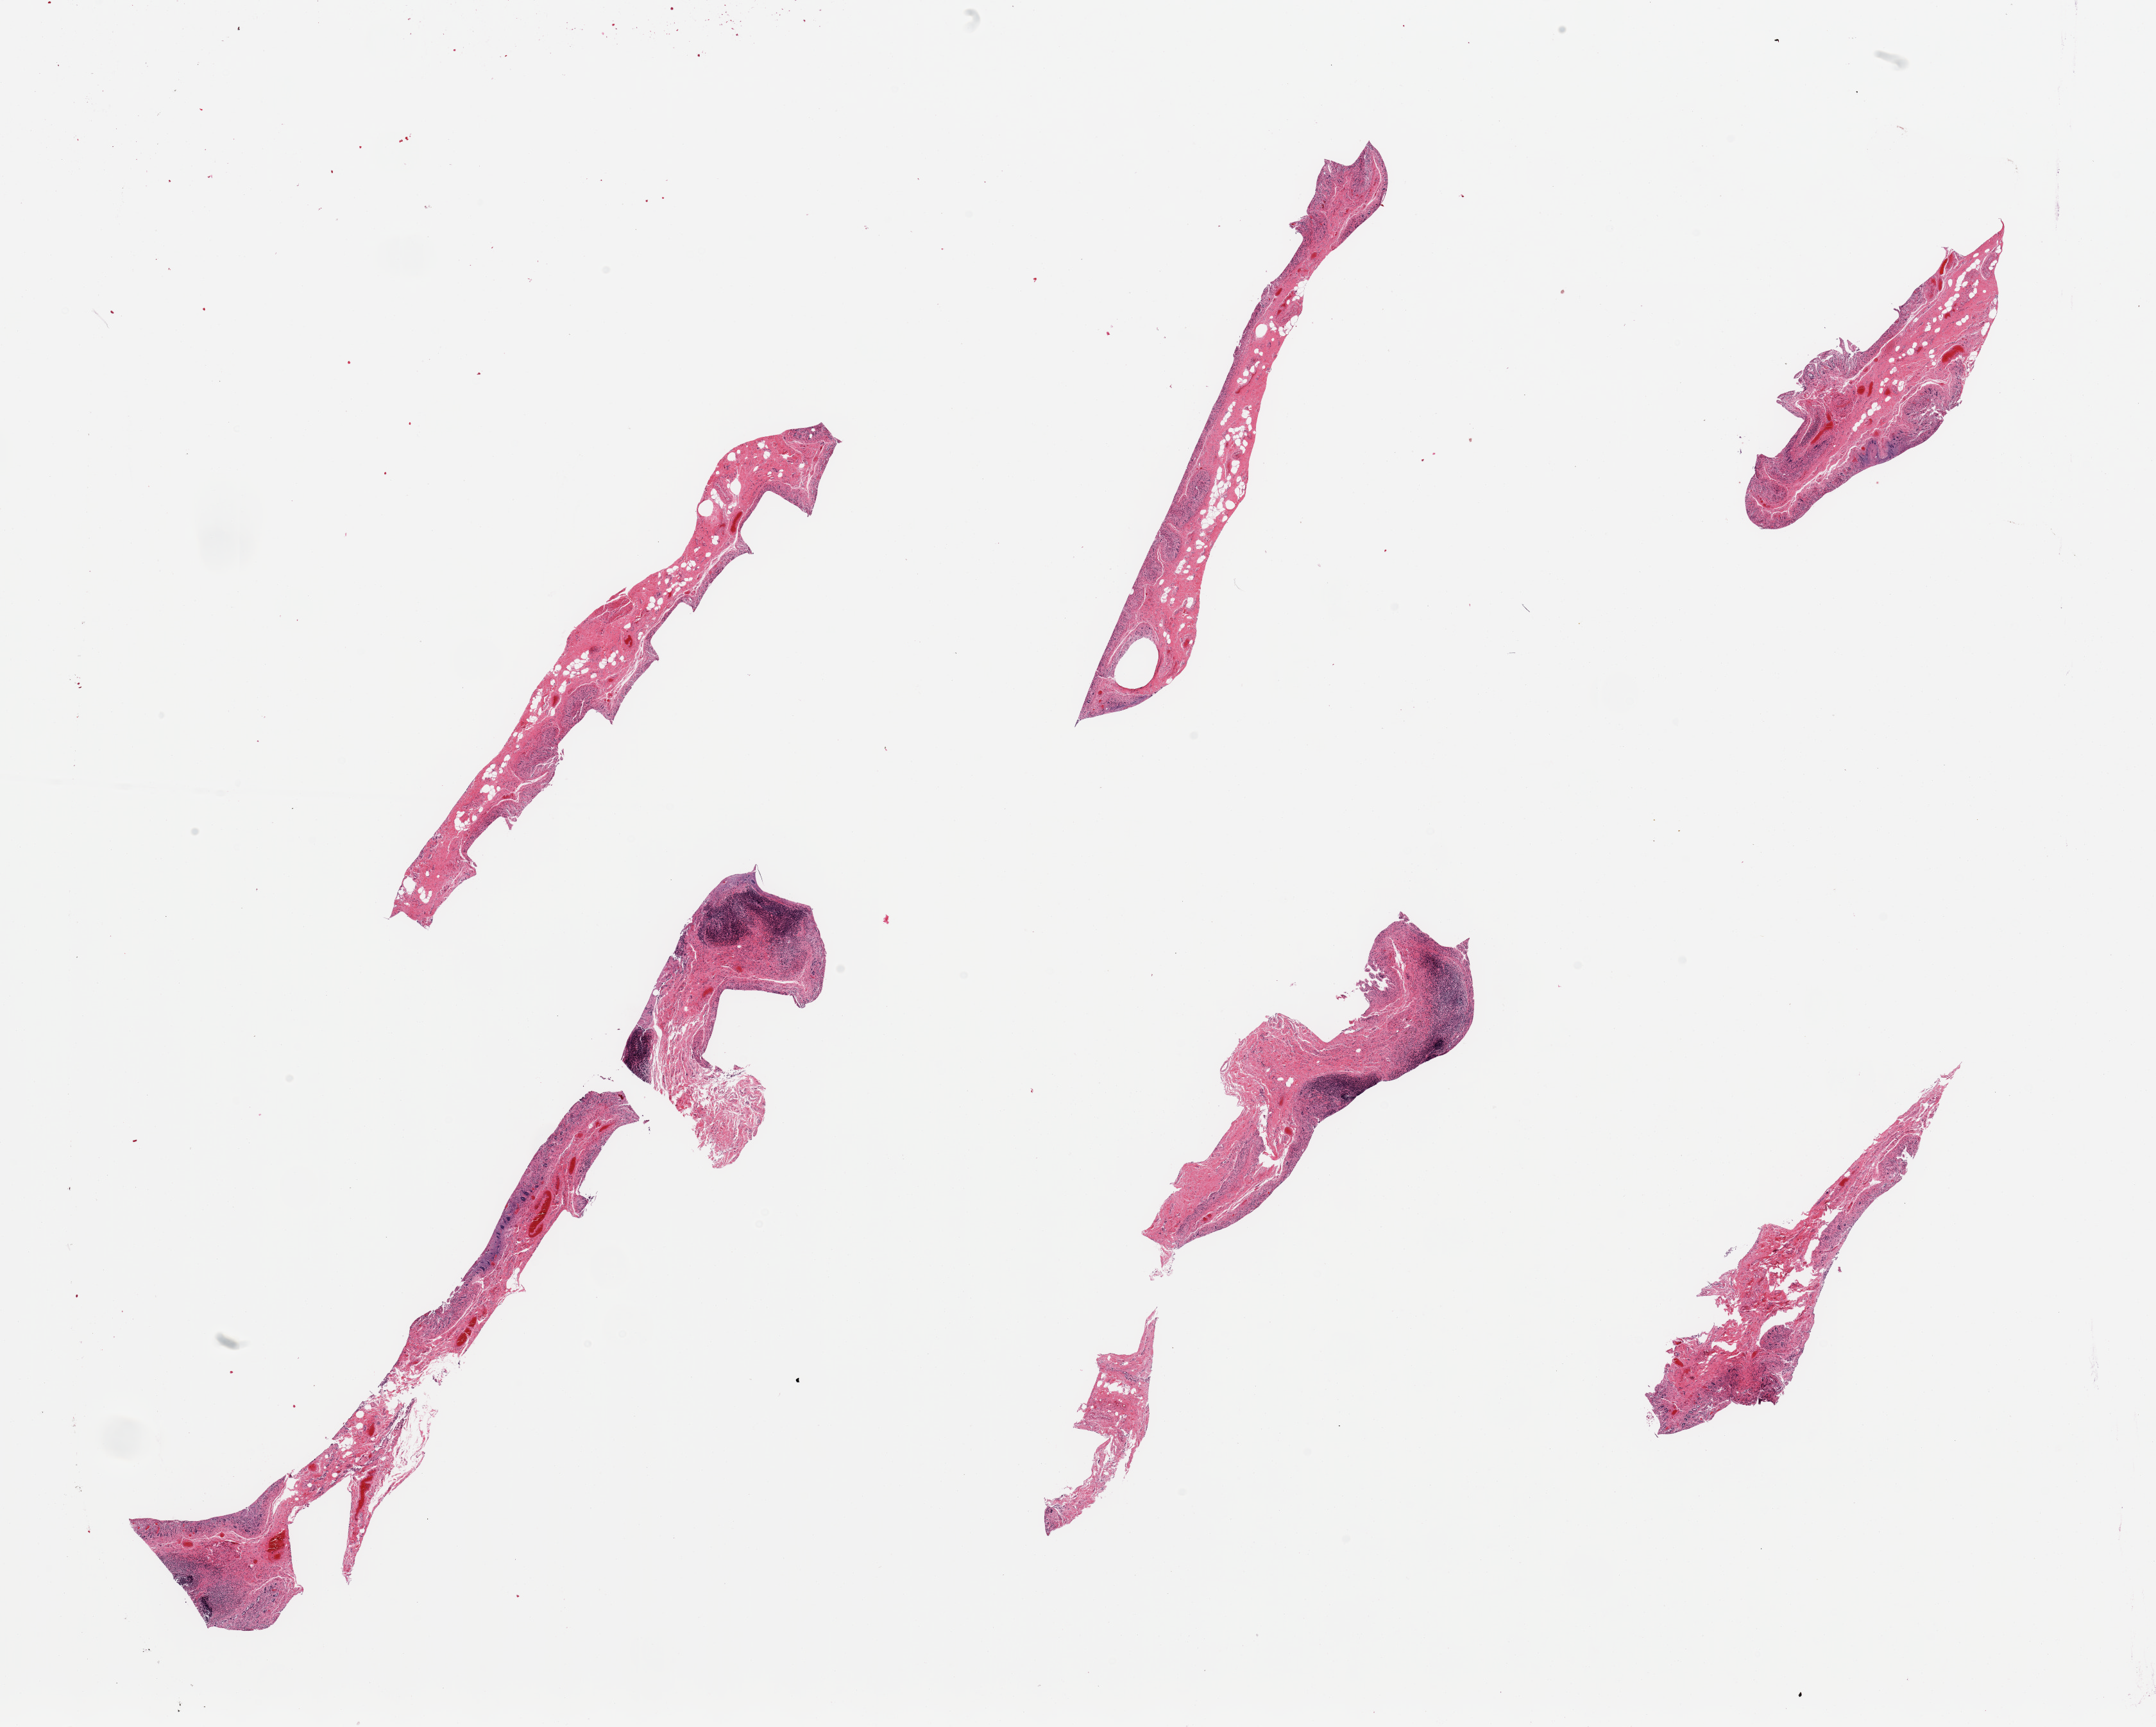
H&E whole-slide image, brightfield — shown as a low-resolution overview of the whole scanned area (about 26.6 x 21.3 mm). PAXgene-fixed paraffin-embedded (PFPE) section. Sampled site (target tissue): ileum. Donor tissue sample. Donor sex: male.
Review note (as recorded): 6 pieces, advanced autolysis, ~10% lymphoid aggregates.